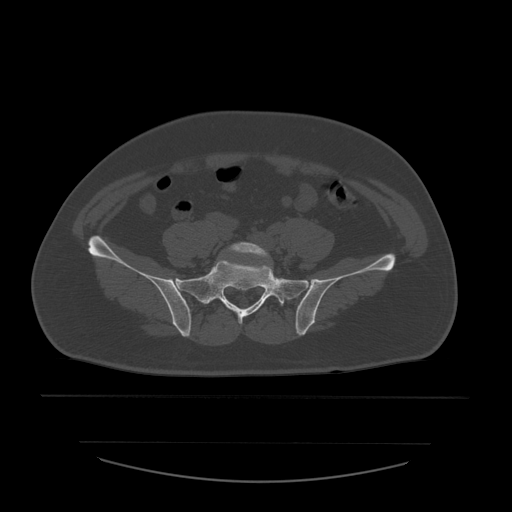
CT including the spine, one axial slice; slice 103 of 532 in the series (ordered by position); reconstruction kernel STANDARD; bone window (W 1800 / L 400 HU); 1.25 mm slice thickness; 512 × 512 image matrix, field of view 441 × 441 mm. Patient age 44 years. Case-level facts recorded for this patient, not image findings: primary cancer: soft tissue sarcoma.
Outlined on this slice (semi-automatic segmentation, software-assisted and operator-edited):
- L5 vertebra: bounding box <227,242,270,261> (left, top, right, bottom; pixels)